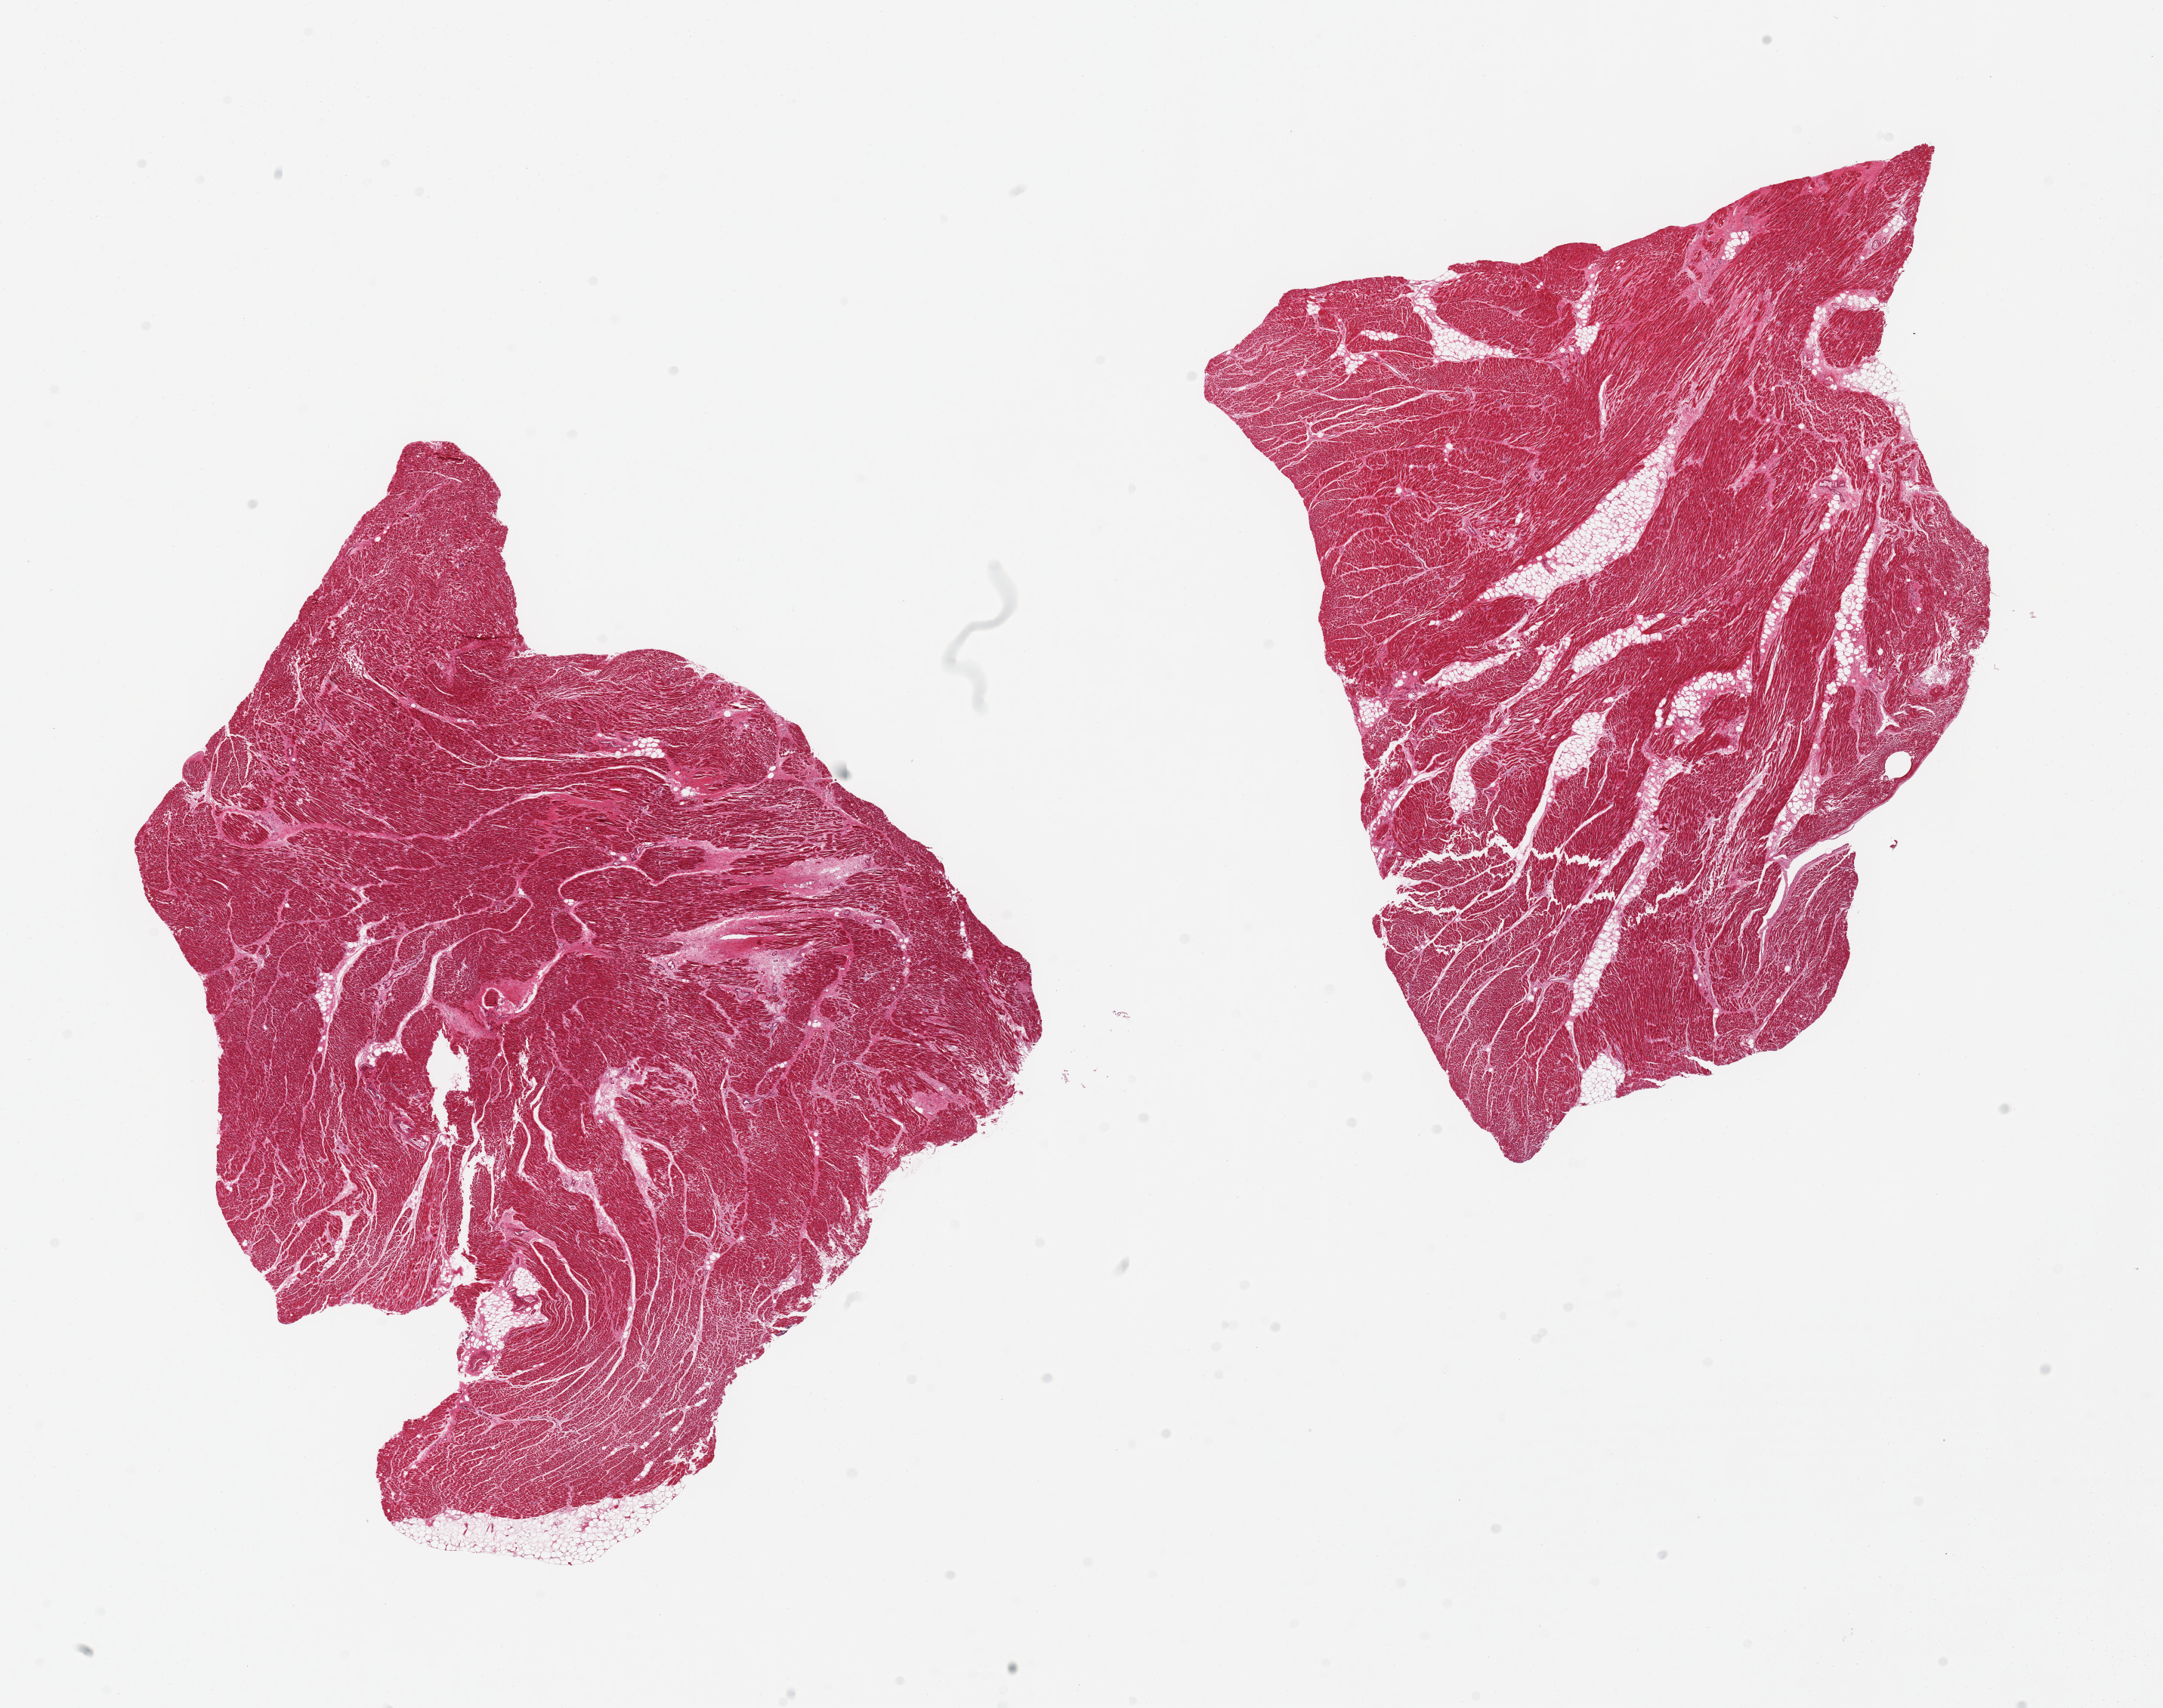
H&E whole-slide image — low-resolution overview of the scanned area, about 22.6 x 17.9 mm (acquisition: 20x scan). PAXgene-fixed paraffin-embedded (PFPE) section. Target tissue: heart. Donor tissue sample. Male donor.
- pathologist's review note for this sample: 2 pieces, 9x9 and 9x8mm; several remote infarcts, ~1x0.5m,m